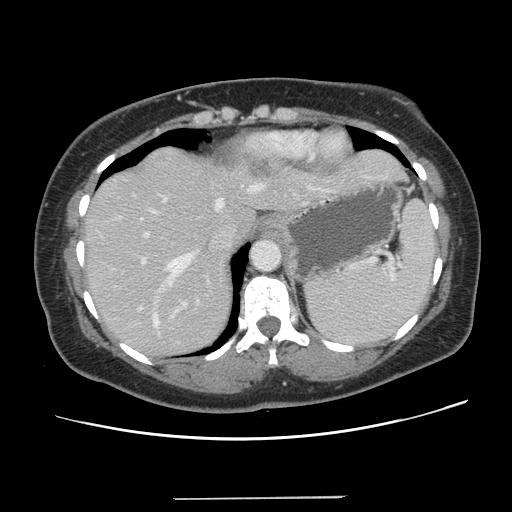
Contrast-enhanced abdominal CT, one axial slice. Position 104 of 141 along the scan axis. Intravenous contrast given. Soft-tissue window (W 400 / L 40 HU). 512 × 512 image matrix, field of view 366 × 366 mm. Female patient, age 53 years. From the clinical record (not read from this slice): diagnosis: colorectal cancer liver metastases, imaged before liver resection; multiple liver metastases: no; largest metastasis: 14.5 cm.
Outlined on this slice (manually delineated by an expert):
- hepatic veins: box from (x=149, y=180) to (x=267, y=327) px
- liver: (x=85, y=147)–(x=403, y=358)
- planned liver remnant (the part of the liver to remain after resection): (x=85, y=209)–(x=257, y=358)
- portal vein (with intrahepatic branches): (x=116, y=188)–(x=313, y=319)